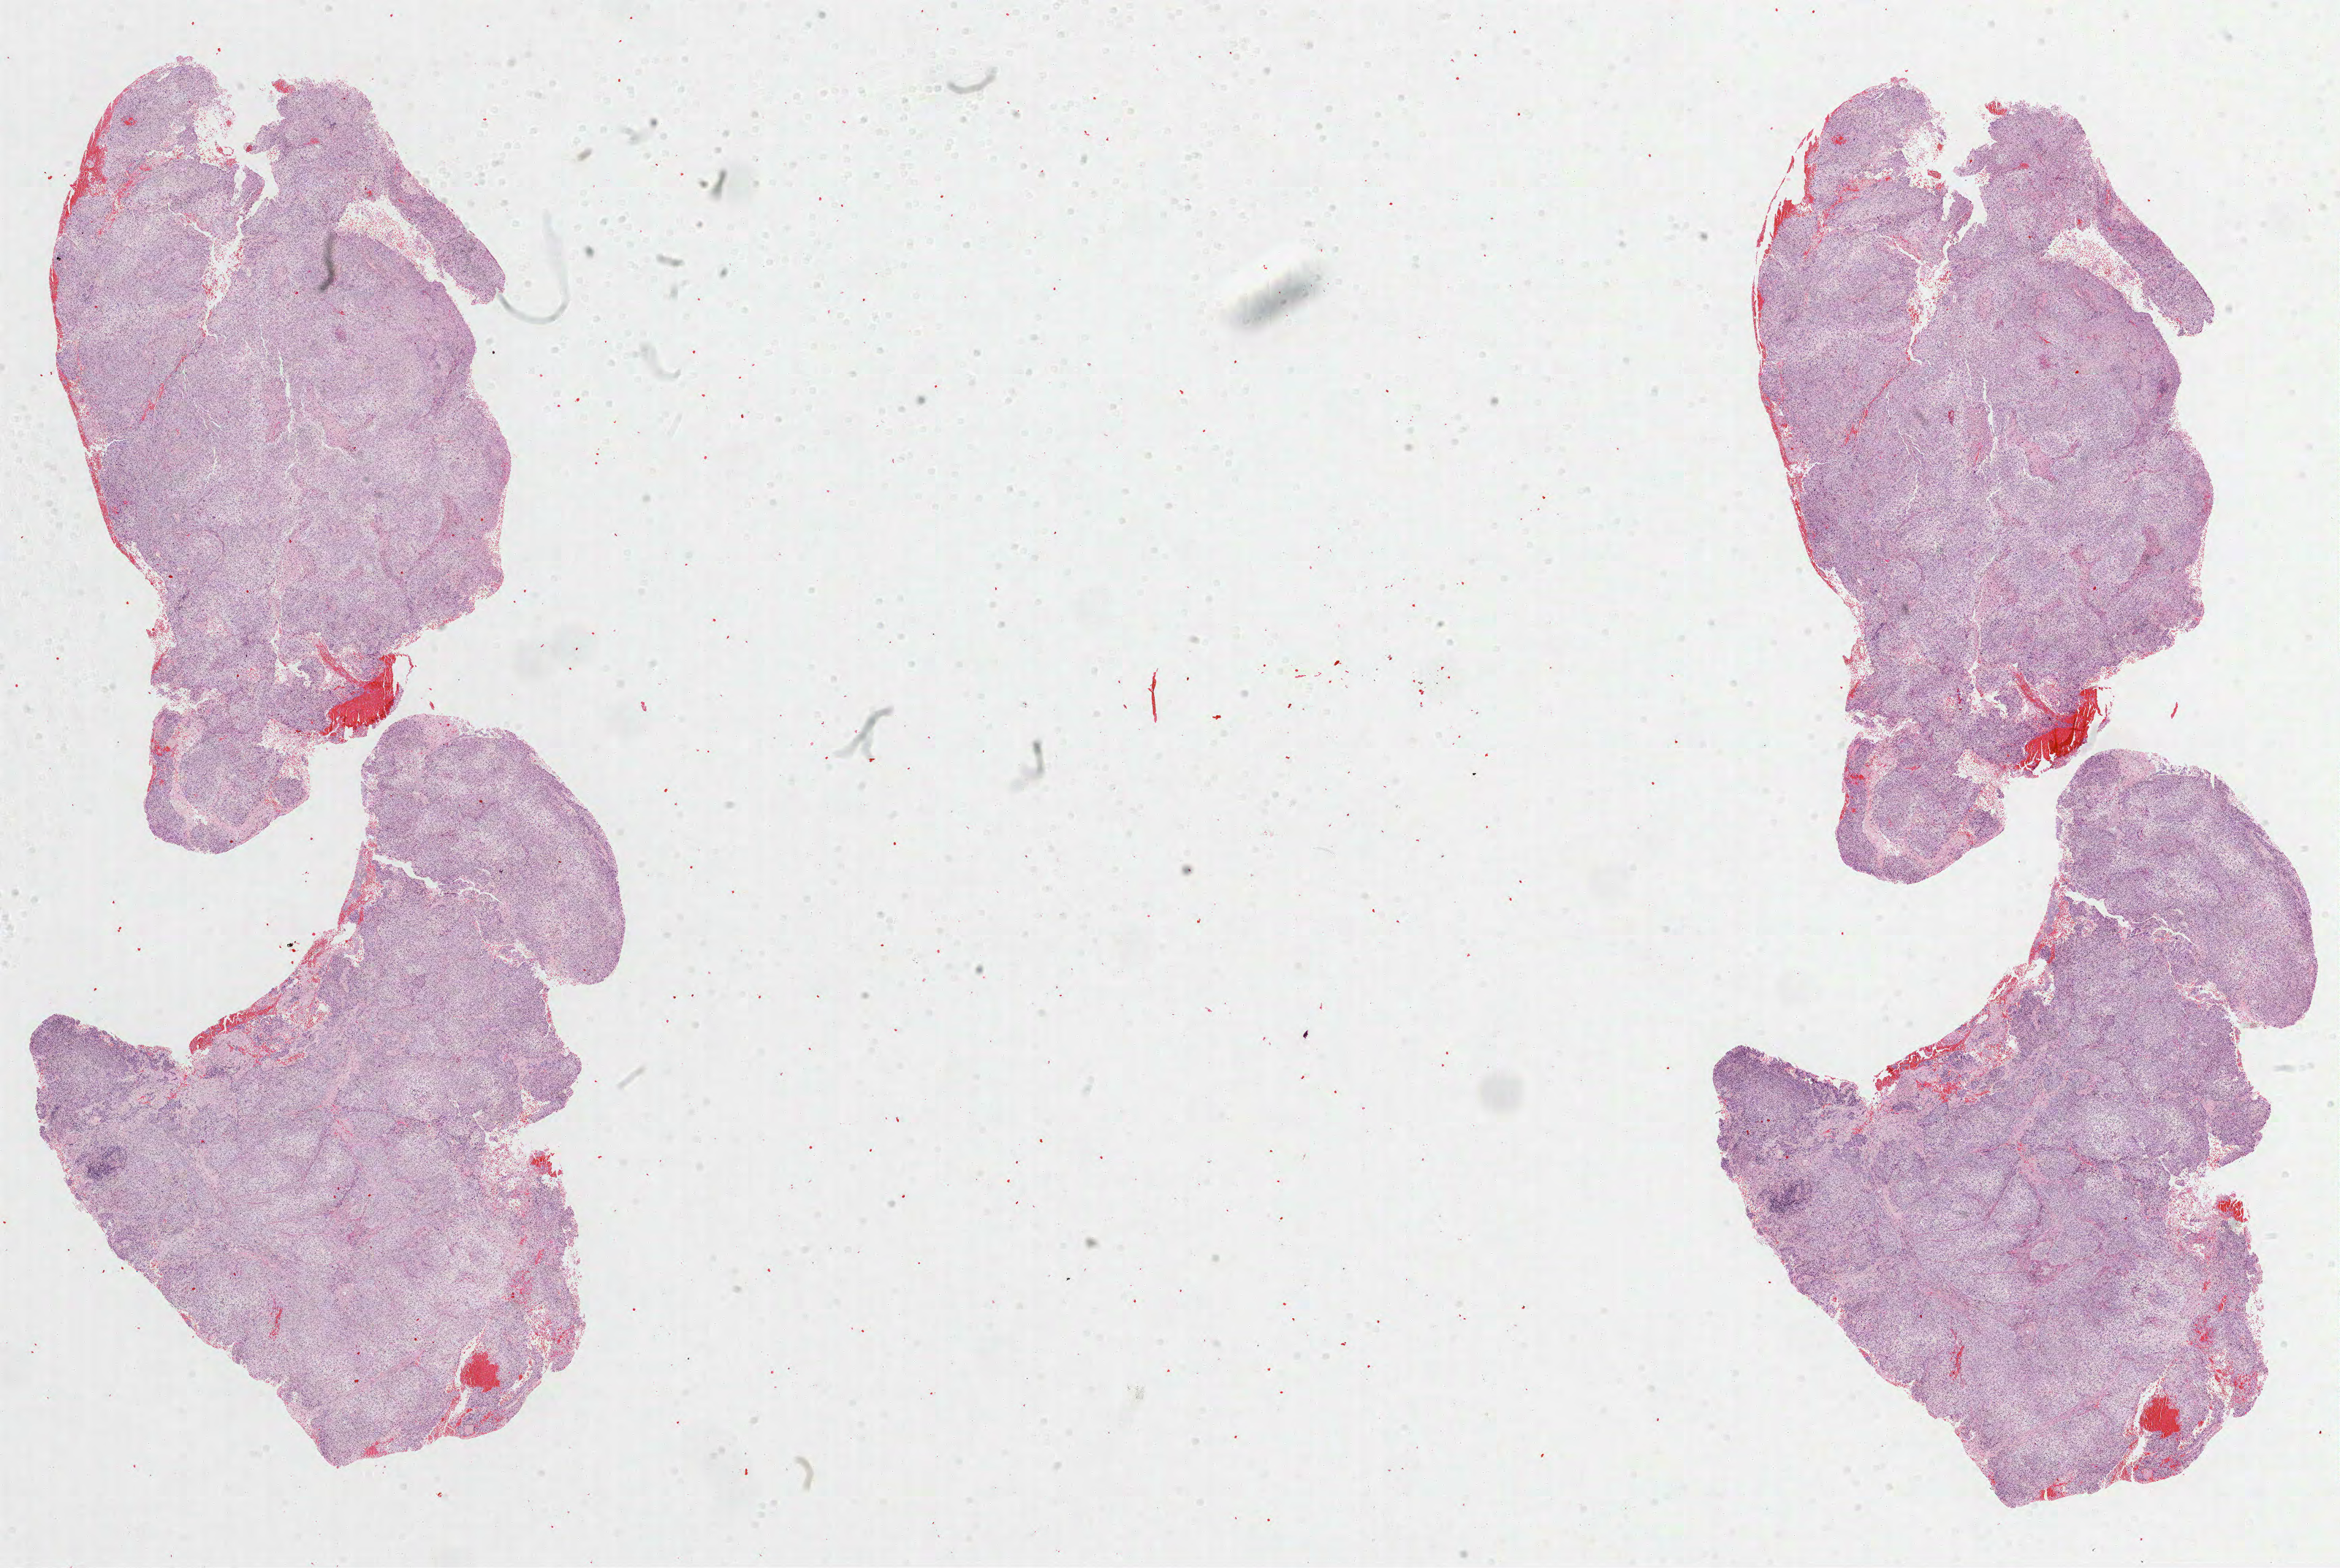
Digitized Hematoxylin and eosin (H&E) stained tissue section (whole slide) — shown as a low-resolution overview of the whole scanned area (about 25.8 x 17.3 mm), FFPE section, cervix, primary tumour sample. Patient: female, age at initial diagnosis 34 years.
Histologic diagnosis: Squamous cell carcinoma, large cell, nonkeratinizing, NOS. FIGO stage: IB2.